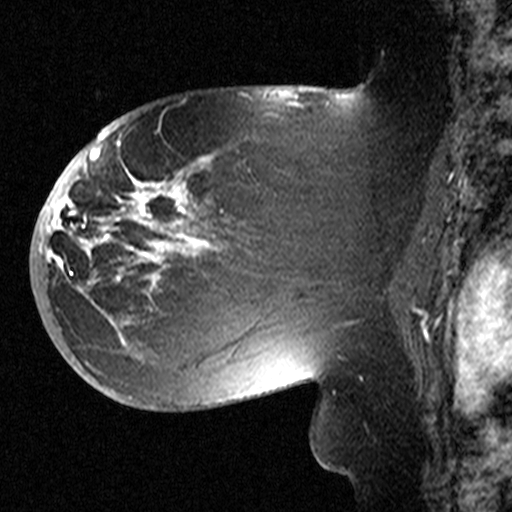
Breast MRI (dynamic contrast-enhanced), one sagittal slice; position 26 of 44 along the scan axis; dynamic contrast-enhanced study with each time point stored as its own series, time point 2 of 3 at this slice position (early post-contrast, ordered by acquisition time); 1.5 T; TE 4.5 ms, TR 11 ms; 512 × 512 image matrix. Female patient, age 53 years. Case-level facts recorded for this patient, not image findings: setting: breast cancer imaged before/during neoadjuvant chemotherapy; receptor status: HR-positive, HER2-negative.
Annotated regions visible in this slice (semi-automatic segmentation, software-assisted and operator-edited):
- analysis volume of interest (the breast-tissue region the enhancement analysis was run in; not a lesion): bounding box [x1, y1, x2, y2] px = [58, 154, 311, 367]
- tumour enhancement mask (voxels above the 90 % enhancement threshold inside the analysis volume of interest): [58, 159, 208, 323]